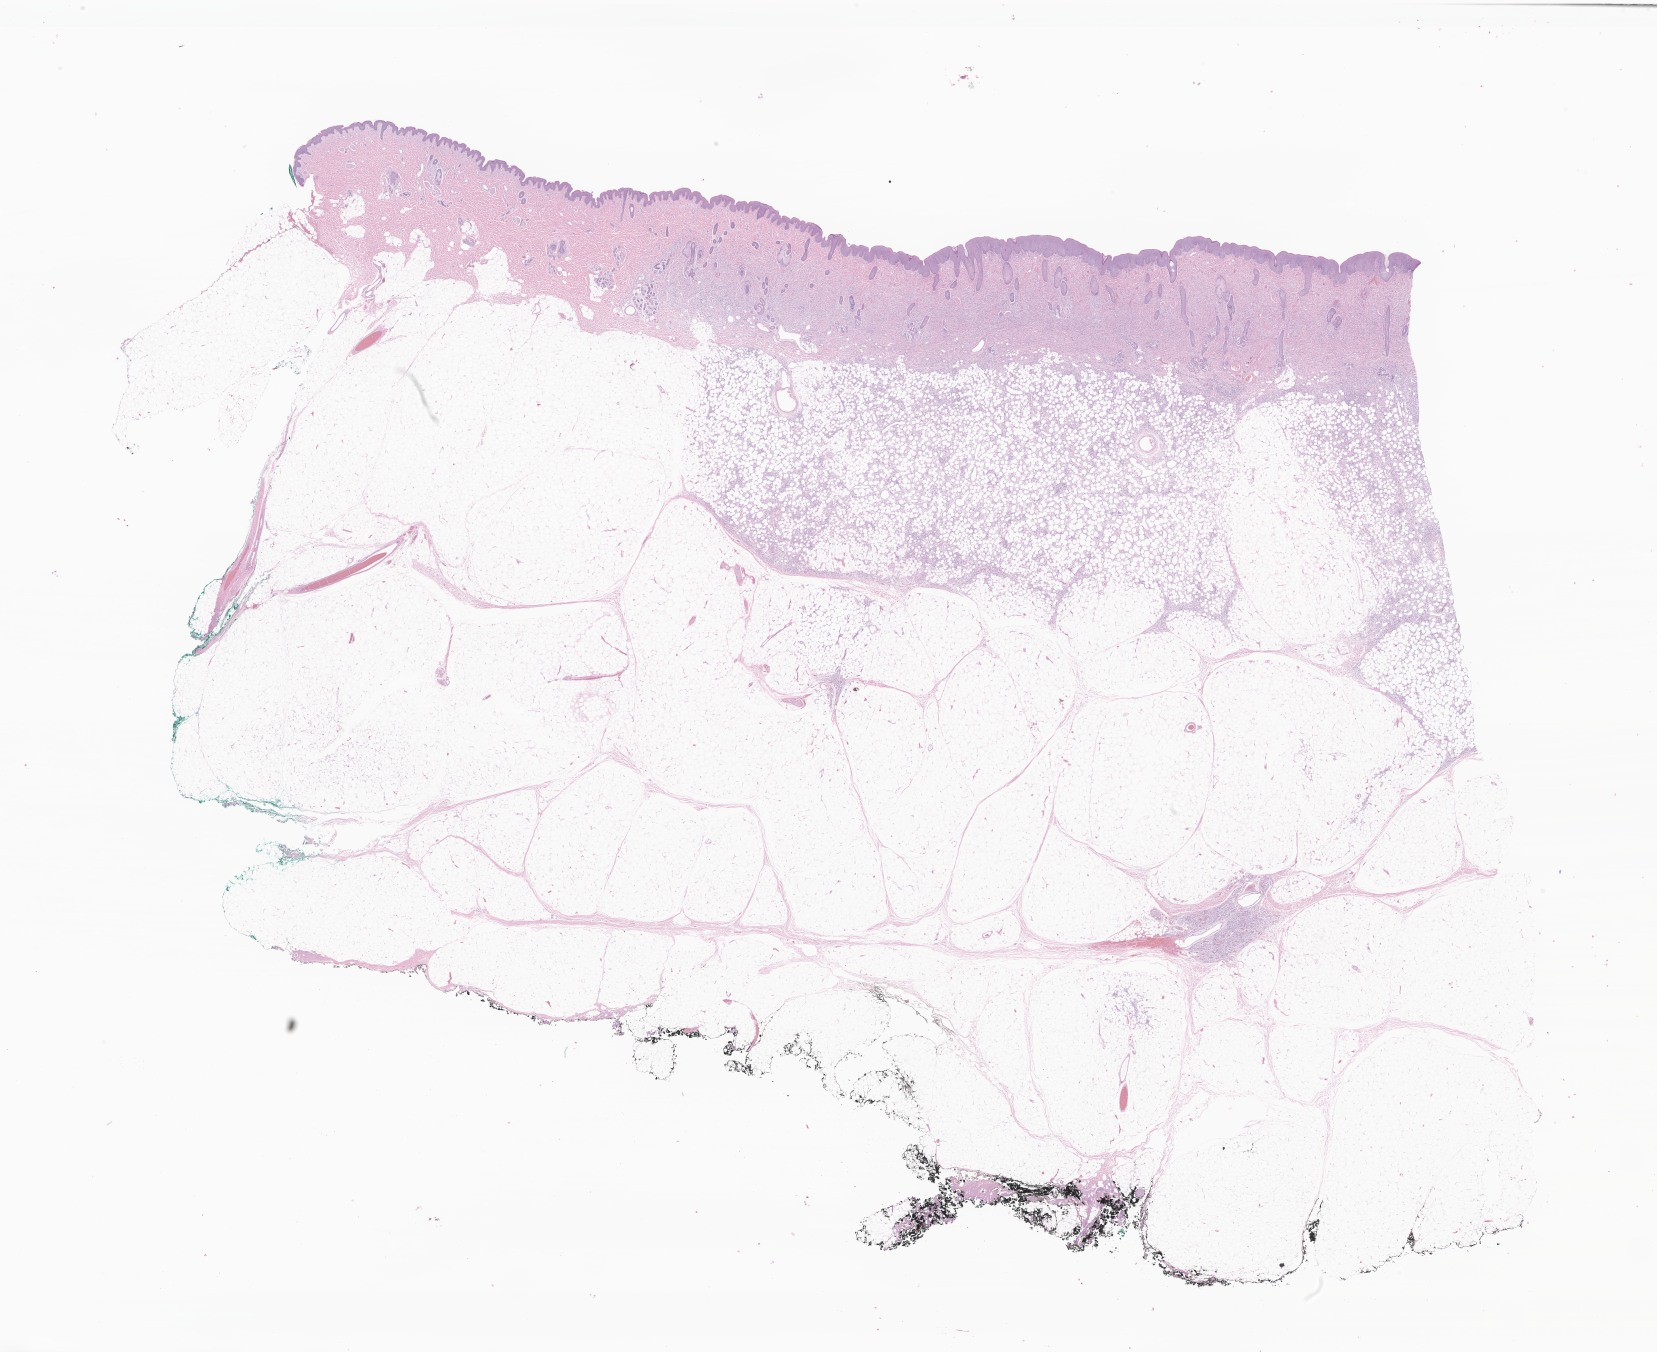
Whole-slide image, haematoxylin and eosin stain of tumor tissue from the skin — a low-resolution overview of the entire scanned area, about 27.9 x 22.8 mm; formalin-fixed paraffin-embedded section. Female patient, age 174 days.
Diagnosis: Malignant tumor, spindle cell type.